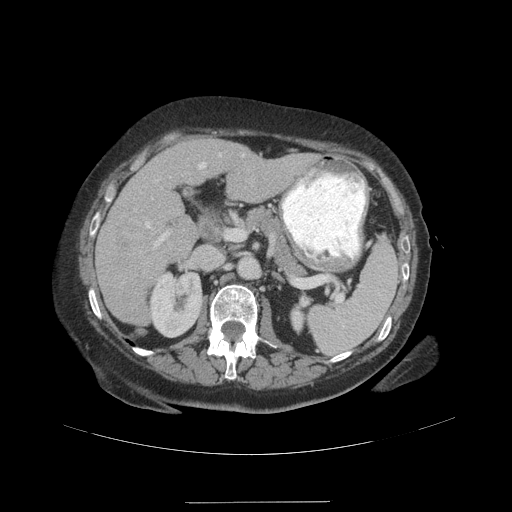
Contrast-enhanced abdominal CT (liver protocol), one axial slice. Slice 58 of 99 in the series (ordered by position). Reconstruction kernel STANDARD. 140 kVp. Soft-tissue window (W 400 / L 40 HU). 2.5 mm slice thickness. 512 × 512 image matrix, field of view 440 × 440 mm. From the clinical record (not read from this slice): diagnosis: hepatocellular carcinoma (patient treated with transarterial chemoembolisation; whether this scan precedes or follows treatment is not stated here); TNM stage (as recorded): Stage-IVA; Child-Pugh class: A; tumour nodularity: multinodular.
Outlined on this slice (semi-automatic segmentation, software-assisted and operator-edited):
- liver parenchyma outside the tumour (the mass and vessels are separate outlines, so this box may not span the whole liver): box from (x=96, y=138) to (x=318, y=326) px
- mass: (x=116, y=235)–(x=138, y=249)
- liver vessels: (x=145, y=153)–(x=244, y=248)